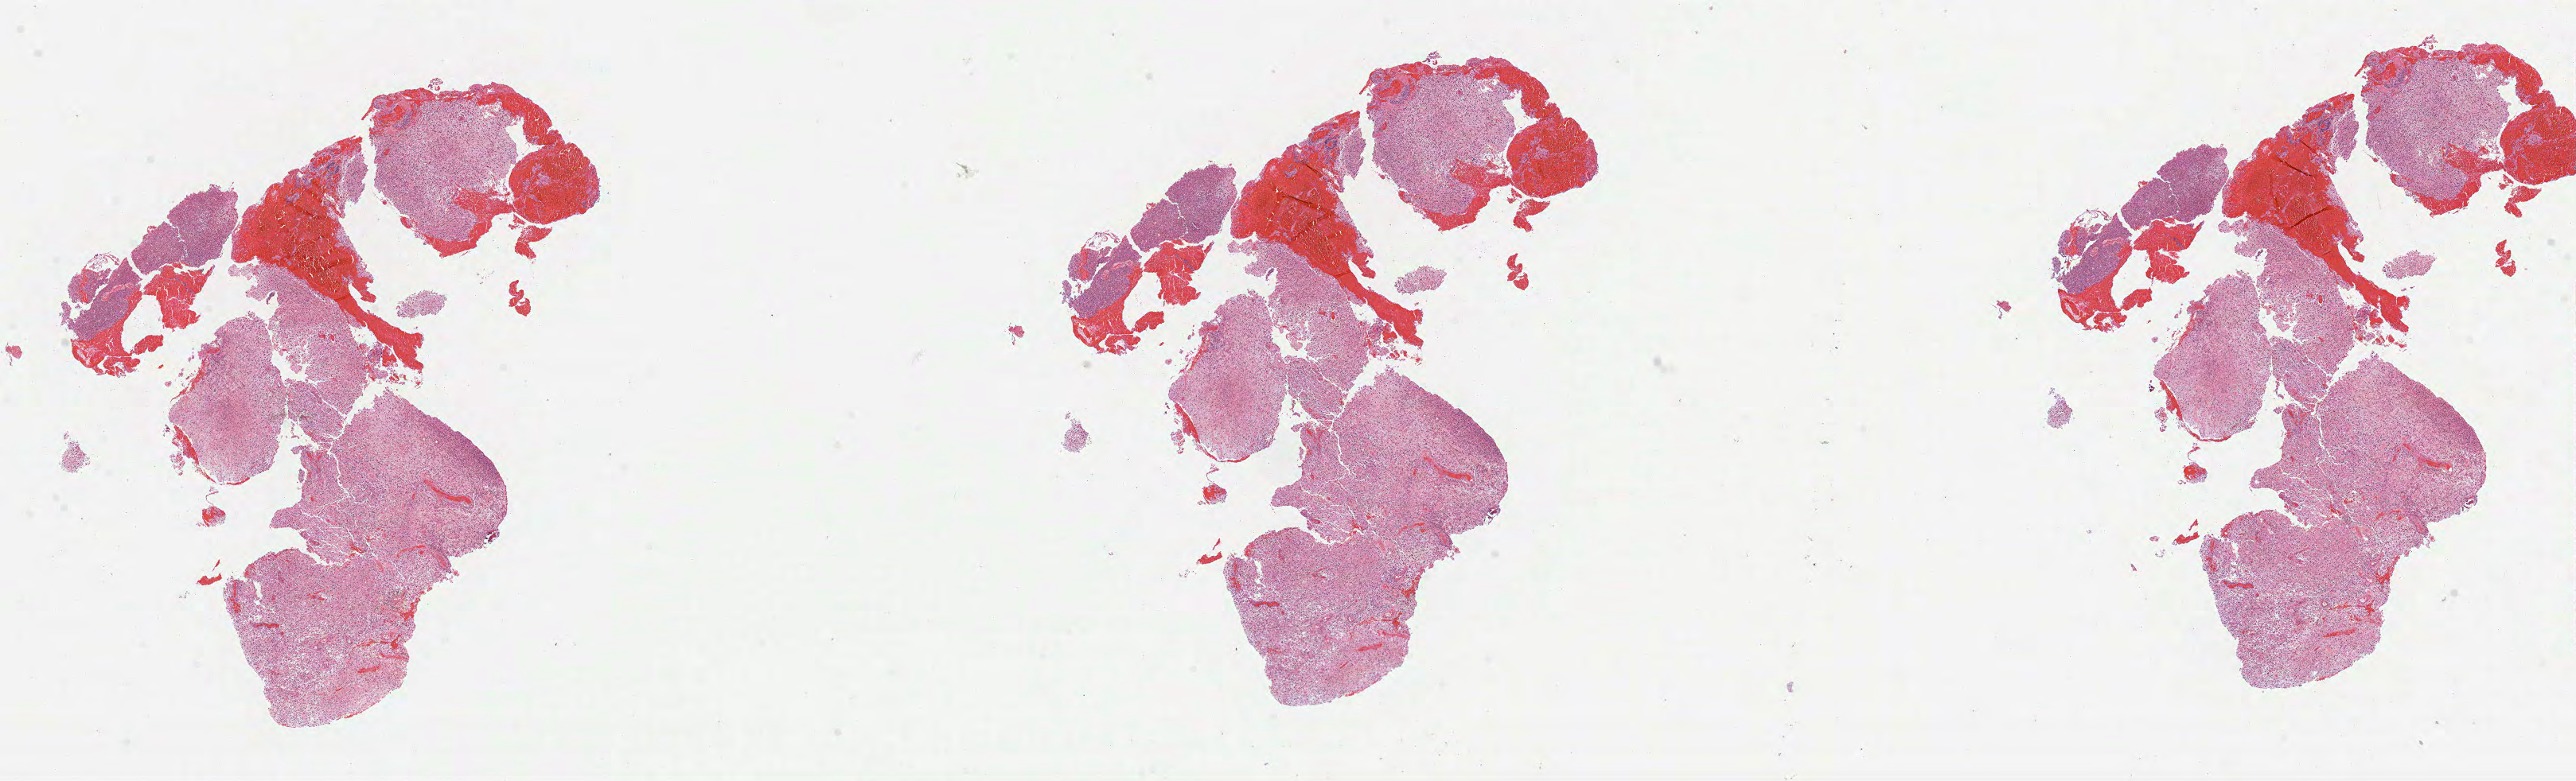
Whole-slide histology image, Hematoxylin and eosin (H&E) stained — whole scanned area (about 26.1 x 7.9 mm, acquisition: 40x scan) shown as a low-resolution overview. FFPE section. Primary tumour sample from the brain. Female patient; age at initial diagnosis 72 years.
Diagnosis: Glioblastoma.